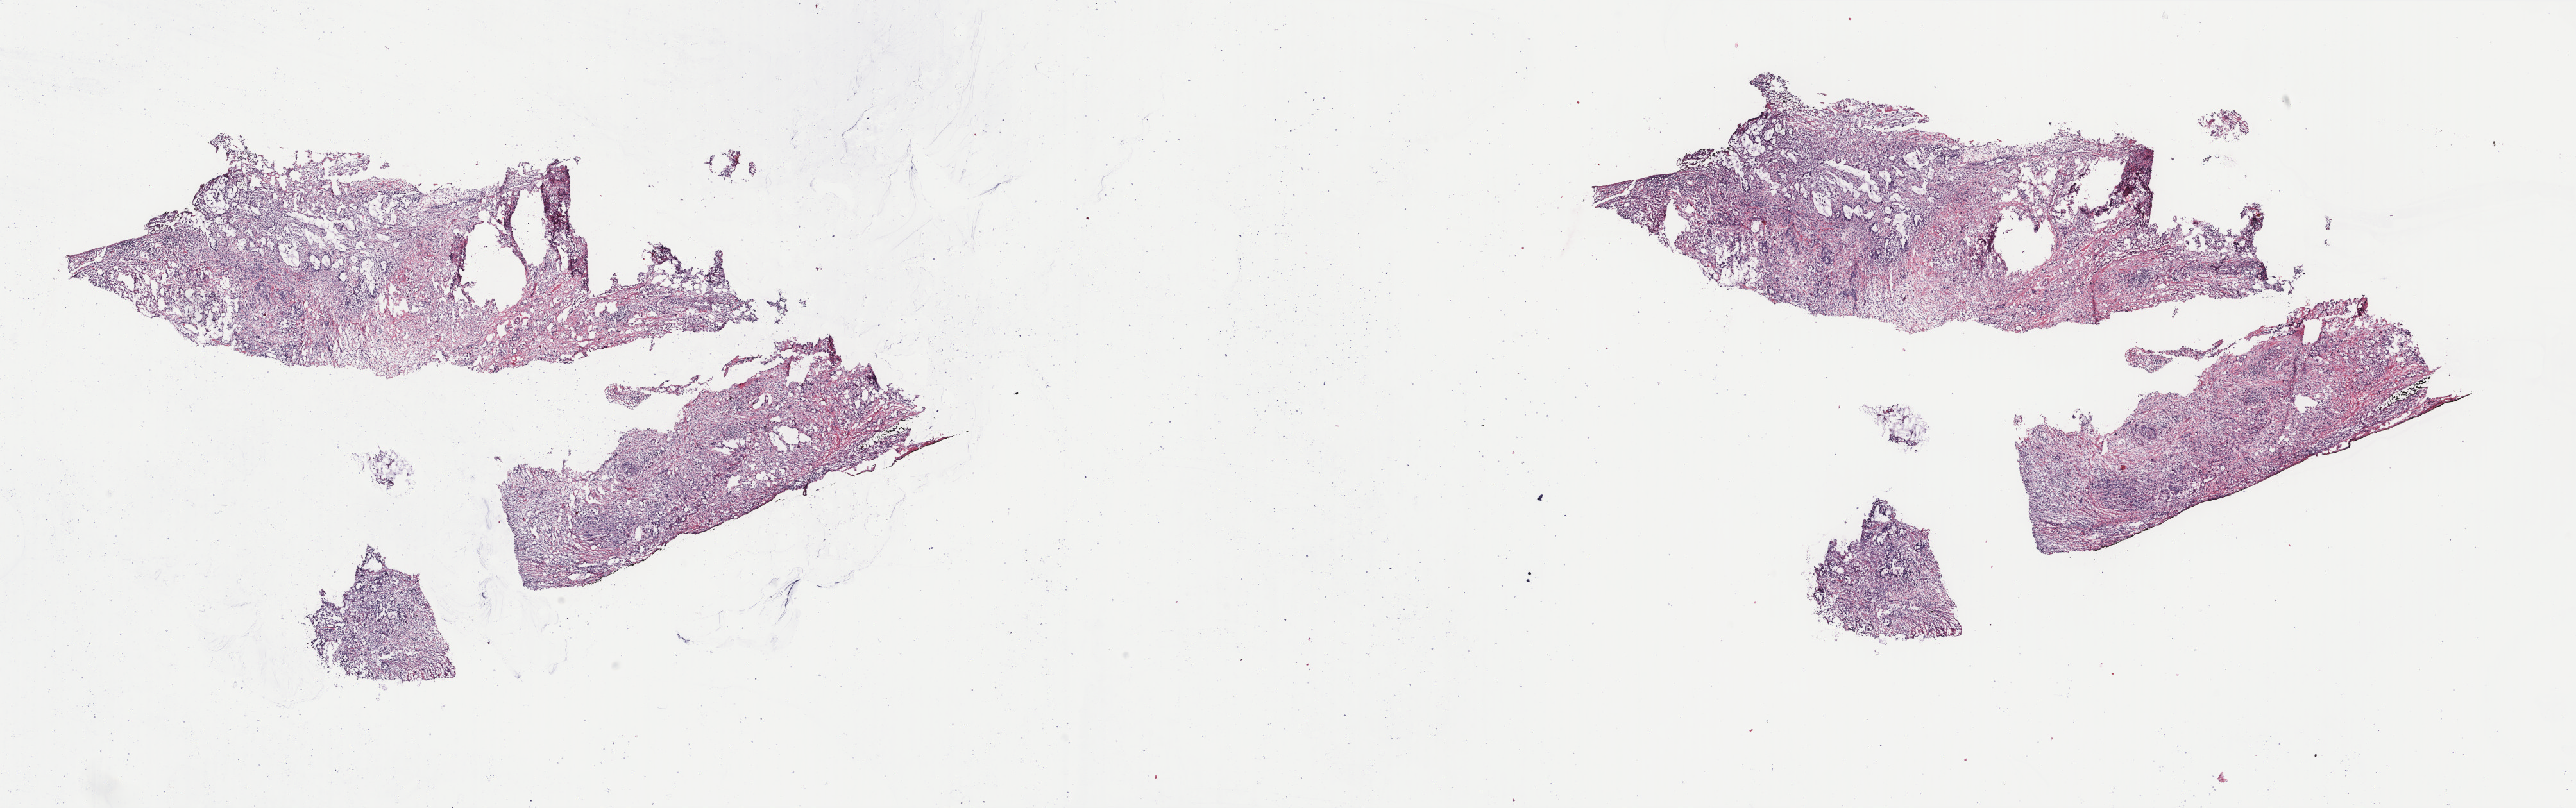
Digitized Hematoxylin and eosin (H&E) stained tissue section (whole slide) — shown as a low-resolution overview of the whole scanned area (about 31.9 x 10.0 mm). Frozen section from the top of the tissue portion. Primary tumour sample from the stomach. Male, age 68 years at initial diagnosis. Histologic grade: G3 (poorly differentiated). Composition of this section per pathologist review: tumour cells 100%, tumour nuclei 70%, normal cells 0%, stromal cells 0%, necrosis 0%. Infiltration values recorded for this section: lymphocyte infiltration 5%, monocyte infiltration 0%, neutrophil infiltration 0%.
* histologic diagnosis: Signet ring cell carcinoma
* TNM: T3 N2 M0
* AJCC pathologic stage: IIIA (7th edition)